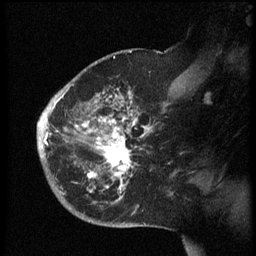
Breast MRI (dynamic contrast-enhanced), one sagittal slice. Position 41 of 60 along the scan axis. Dynamic contrast-enhanced series, image 2 of 3 at this slice position (ordered by acquisition). 1.5 T. TE 4.2 ms, TR 8.4 ms. 2.5 mm slice thickness. 256 × 256 image matrix, field of view 200 × 200 mm. Patient: female, 38 years. From the clinical record (not read from this slice): setting: breast cancer imaged before/during neoadjuvant chemotherapy; receptor status: HER2-positive.
Outlined on this slice (semi-automatically segmented with operator editing):
- analysis volume of interest (the breast-tissue region the enhancement analysis was run in; not a lesion): bounding box (x1, y1, x2, y2) in pixels: (38, 74, 173, 202)
- tumour enhancement mask (voxels above the 70 % enhancement threshold inside the analysis volume of interest): (38, 92, 152, 200)